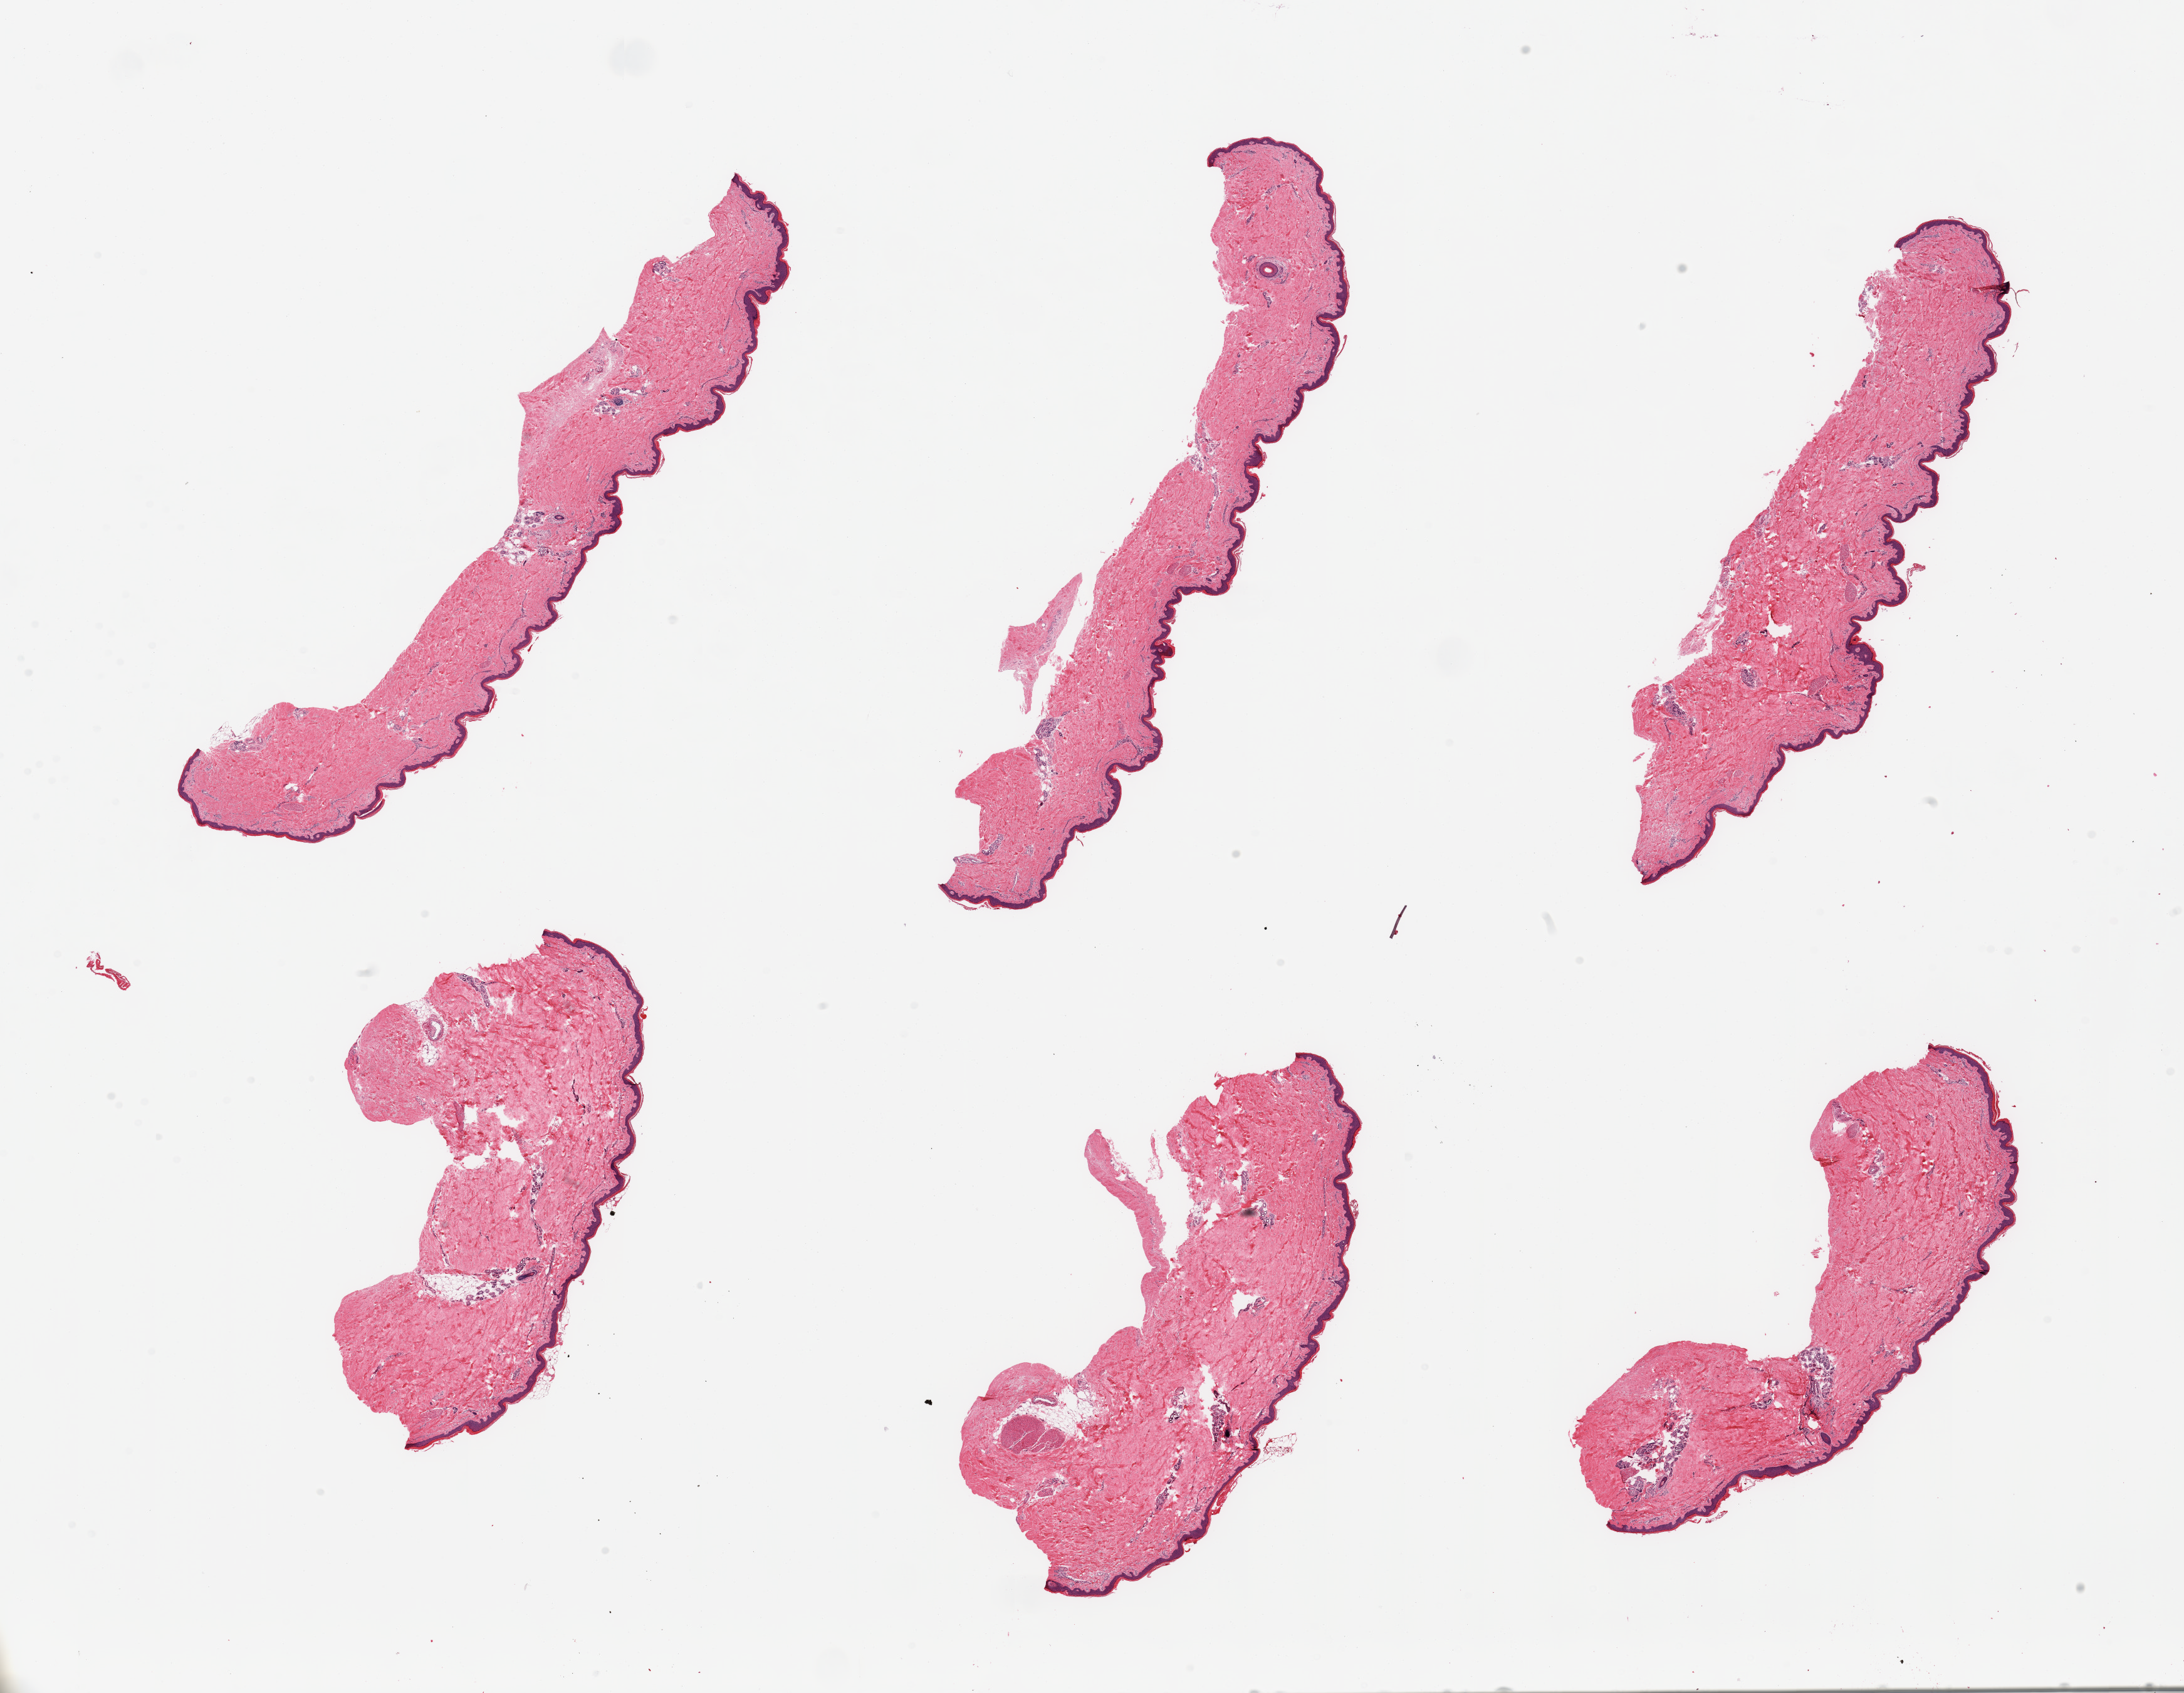
Digitized haematoxylin and eosin-stained section, a low-resolution overview of the entire scanned area, about 27.6 x 21.4 mm. PAXgene-fixed paraffin-embedded (PFPE) section. Section of skin of lower leg (target tissue). Donor tissue sample. Donor sex: male.
Pathologist's review note for this sample: 6 pieces; well trimmed, epidermis measures 37 microns.